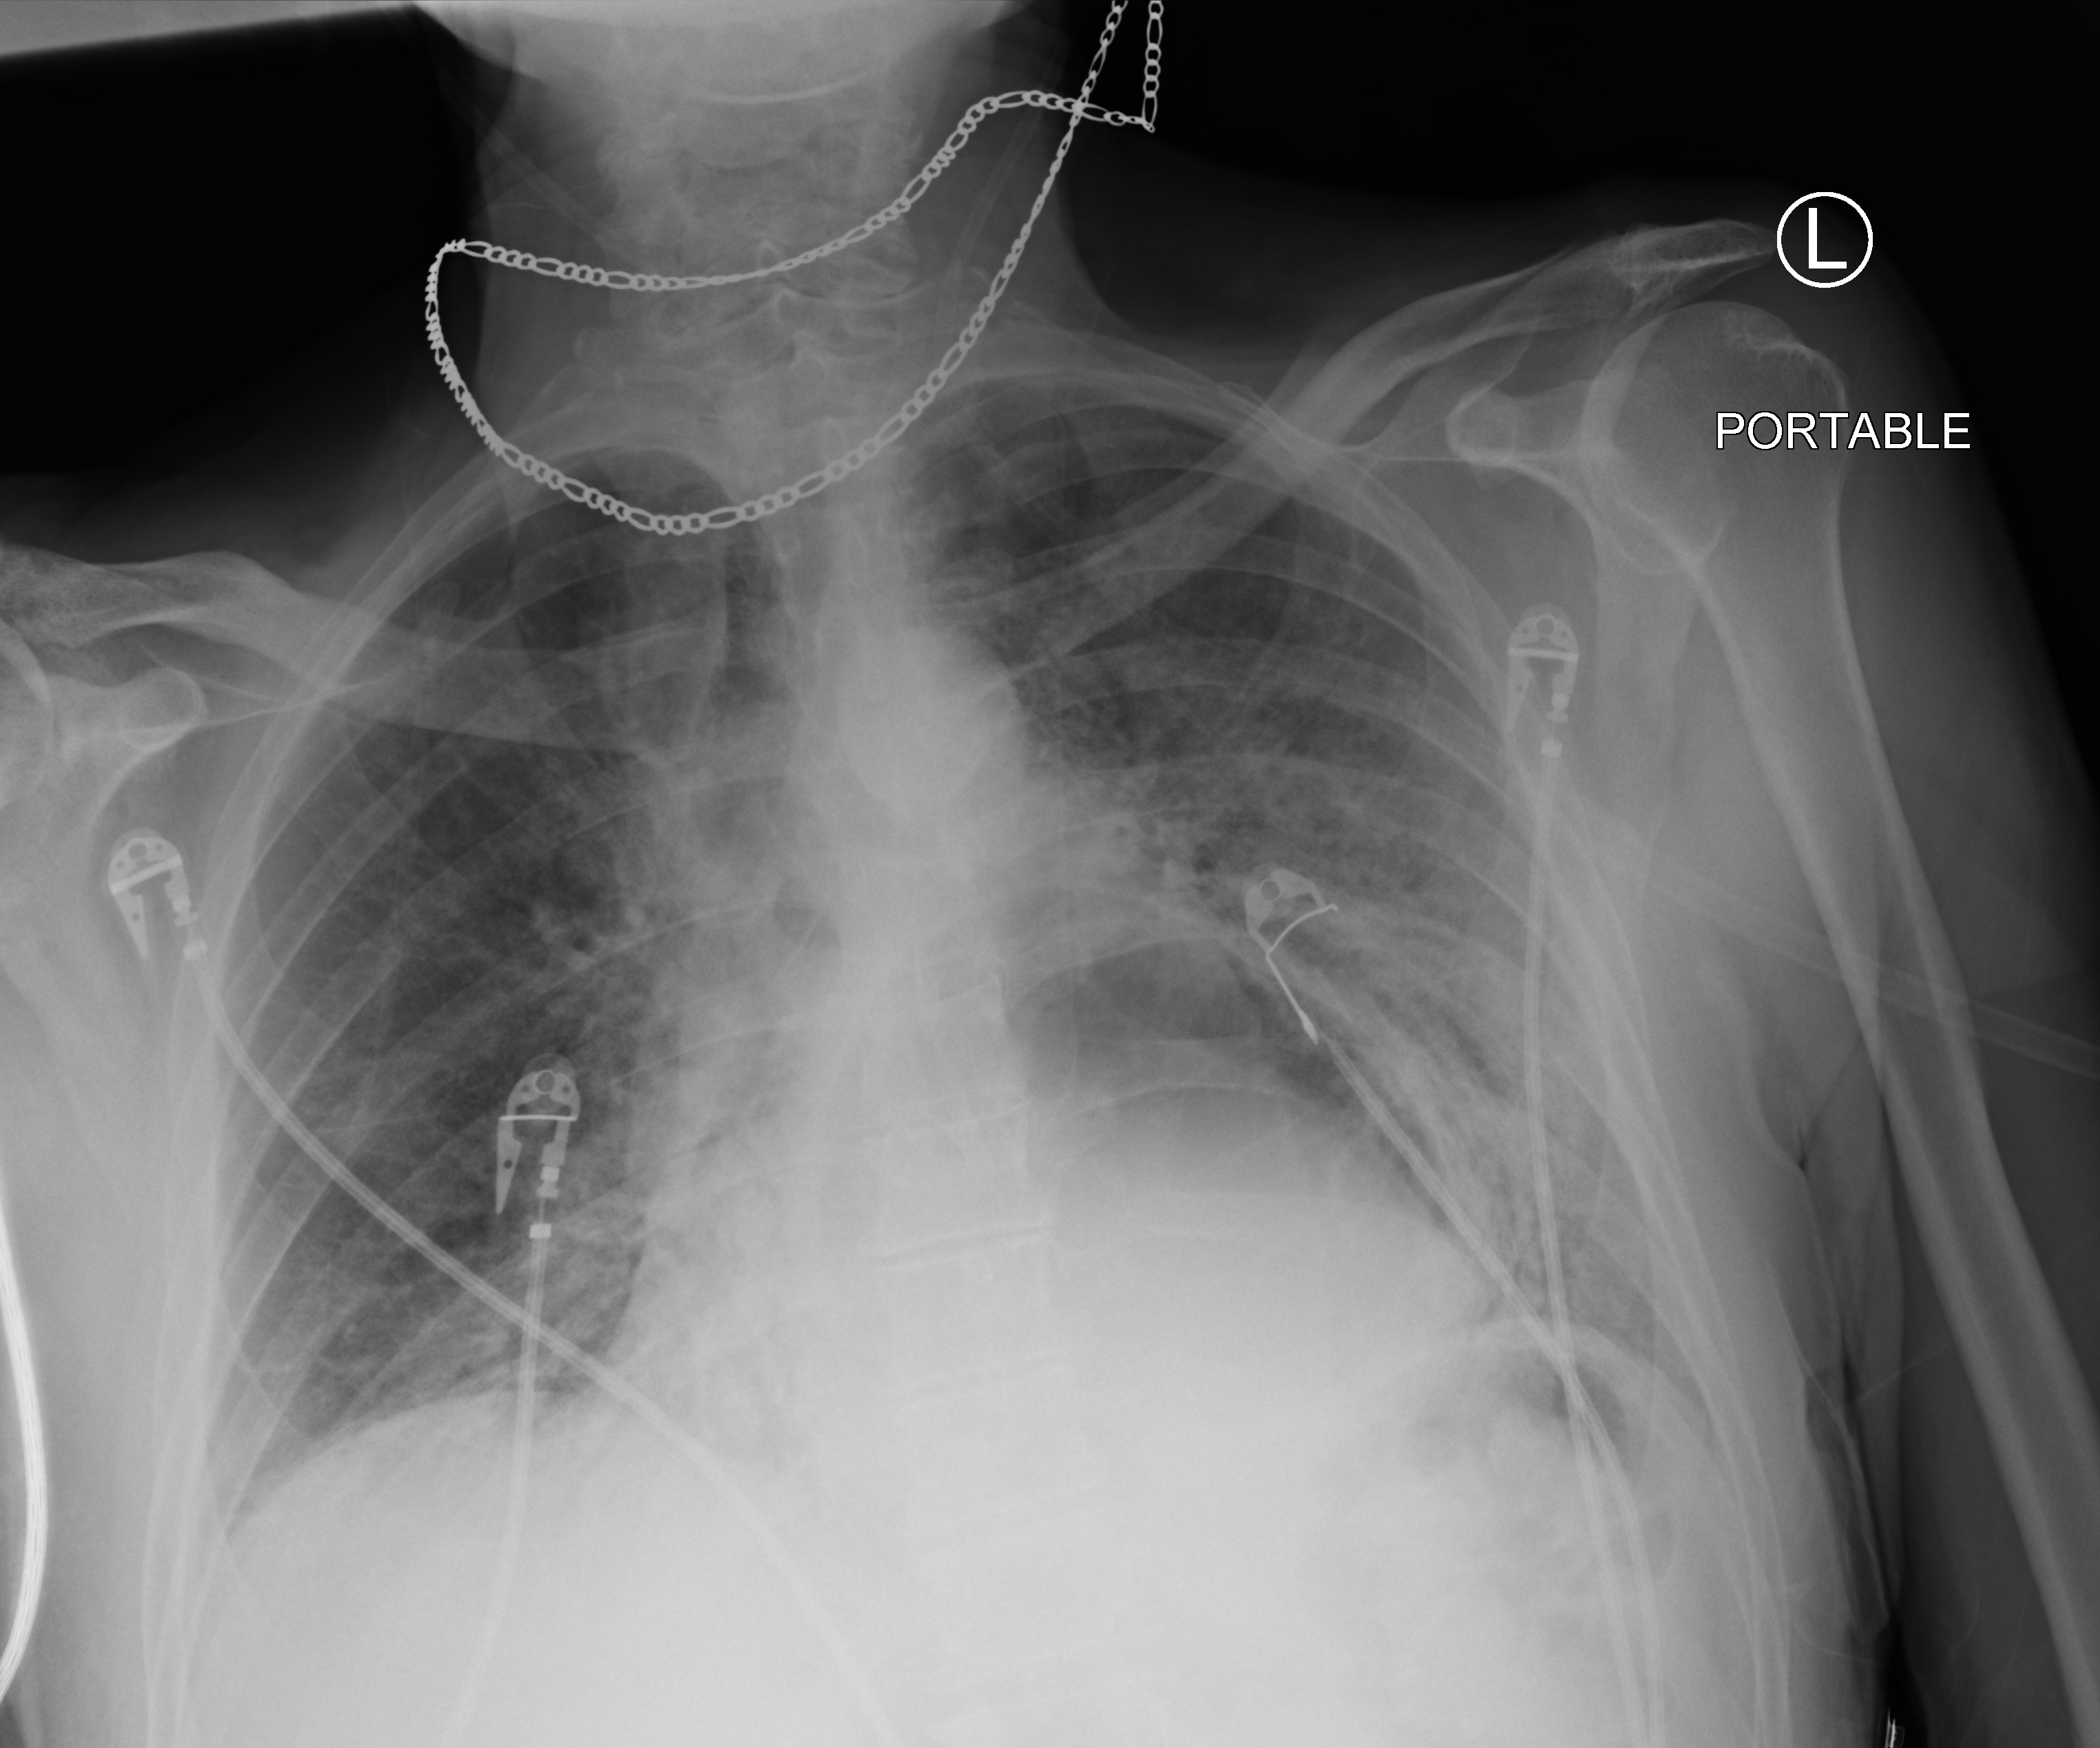
Chest X-ray (portable), anteroposterior (AP) projection. Male patient hospitalised with COVID-19, age 75–90 years.
Hospital-stay facts (about this admission, not read from this image; timing relative to this image not recorded):
- other chronic lung disease (admission record): no
- mechanically ventilated during this hospital stay: yes
- length of hospital stay: 10 days